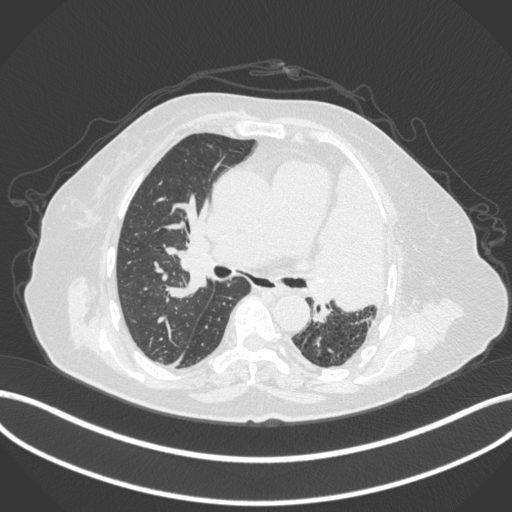
Chest CT, one axial slice. Reconstruction kernel B31f. 120 kVp. Lung window (W 1500 / L -600 HU). 1 mm slice thickness. 512 × 512 image matrix, field of view 400 × 400 mm. Patient: female, 75 years. Case-level facts recorded for this patient, not image findings: clinical TNM (as recorded): T3 N3 M1.
Annotated regions visible in this slice (rectangle marked by the reading radiologist):
- lung tumour (recorded histology: adenocarcinoma): bounding box [x1, y1, x2, y2] px = [303, 152, 387, 314]